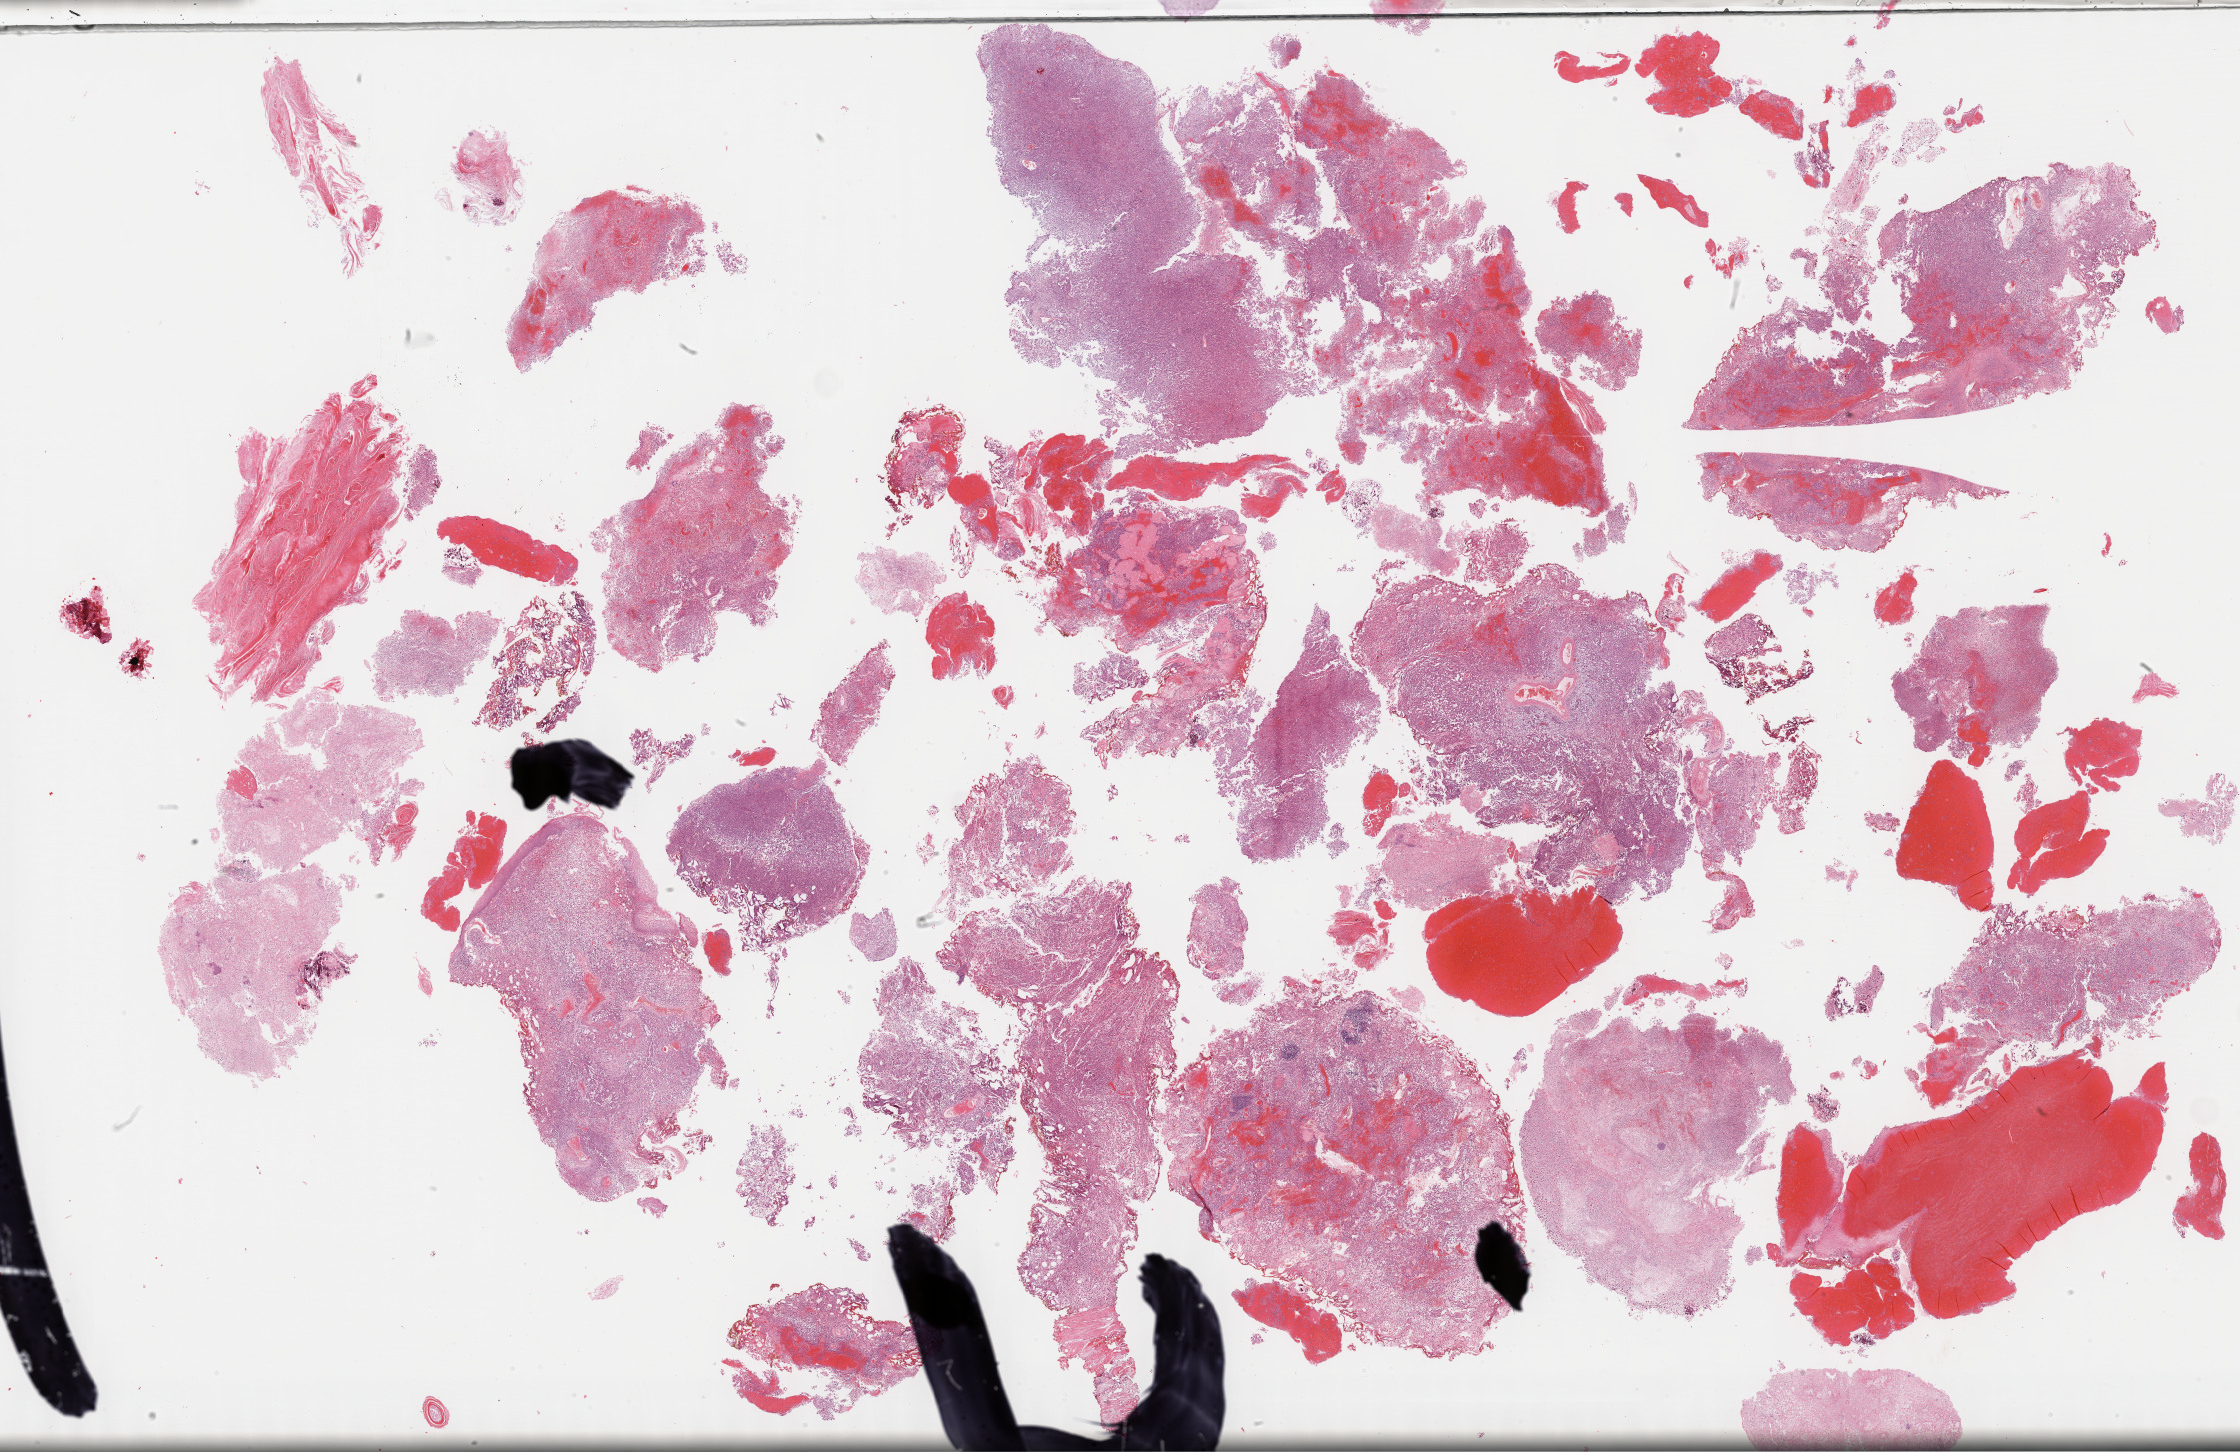
Whole-slide histology image, Hematoxylin and eosin (H&E) stained — a low-resolution overview of the entire scanned area, about 36.2 x 23.5 mm (acquisition: 40x scan); formalin-fixed paraffin-embedded (FFPE) diagnostic section; bladder, primary tumour sample. Patient: male, age at initial diagnosis 74 years. Histologic grade: high grade.
* diagnosis: Carcinoma, NOS
* AJCC pathologic stage: II